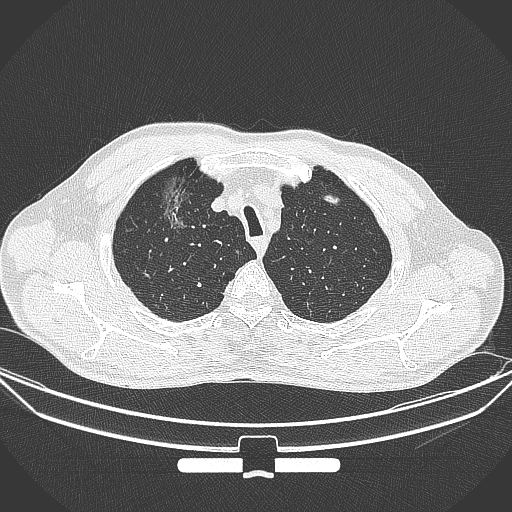
Chest CT, one axial slice; position 290 of 355 along the scan axis; 120 kVp; lung window (W 1500 / L -600 HU); 1 mm slice thickness; 512 × 512 image matrix, field of view 399 × 399 mm. Male patient, age 67 years. Case-level facts recorded for this patient, not image findings: clinical TNM (as recorded): T1c N0 M0; histopathological grade: G2.
Outlined on this slice (bounding box drawn by a radiologist):
- lung tumour (recorded histology: adenocarcinoma): bounding box (x1, y1, x2, y2) in pixels: (157, 176, 200, 243)